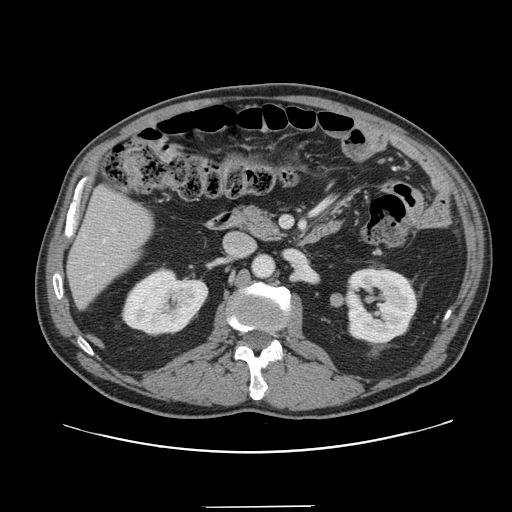
Contrast-enhanced abdominal CT, one axial slice; slice 62 of 139 in the series (ordered by position); soft-tissue window (W 400 / L 40 HU); 2.5 mm slice thickness; 512 × 512 image matrix, field of view 397 × 397 mm. Male patient, age 64 years. From the clinical record (not read from this slice): diagnosis: colorectal cancer liver metastases, imaged before liver resection; multiple liver metastases: yes; largest metastasis: 3.5 cm.
Annotated regions visible in this slice (outlined manually by an expert reader):
- liver: bounding box <68,189,153,306> (left, top, right, bottom; pixels)
- planned liver remnant (the part of the liver to remain after resection): <68,189,153,306>